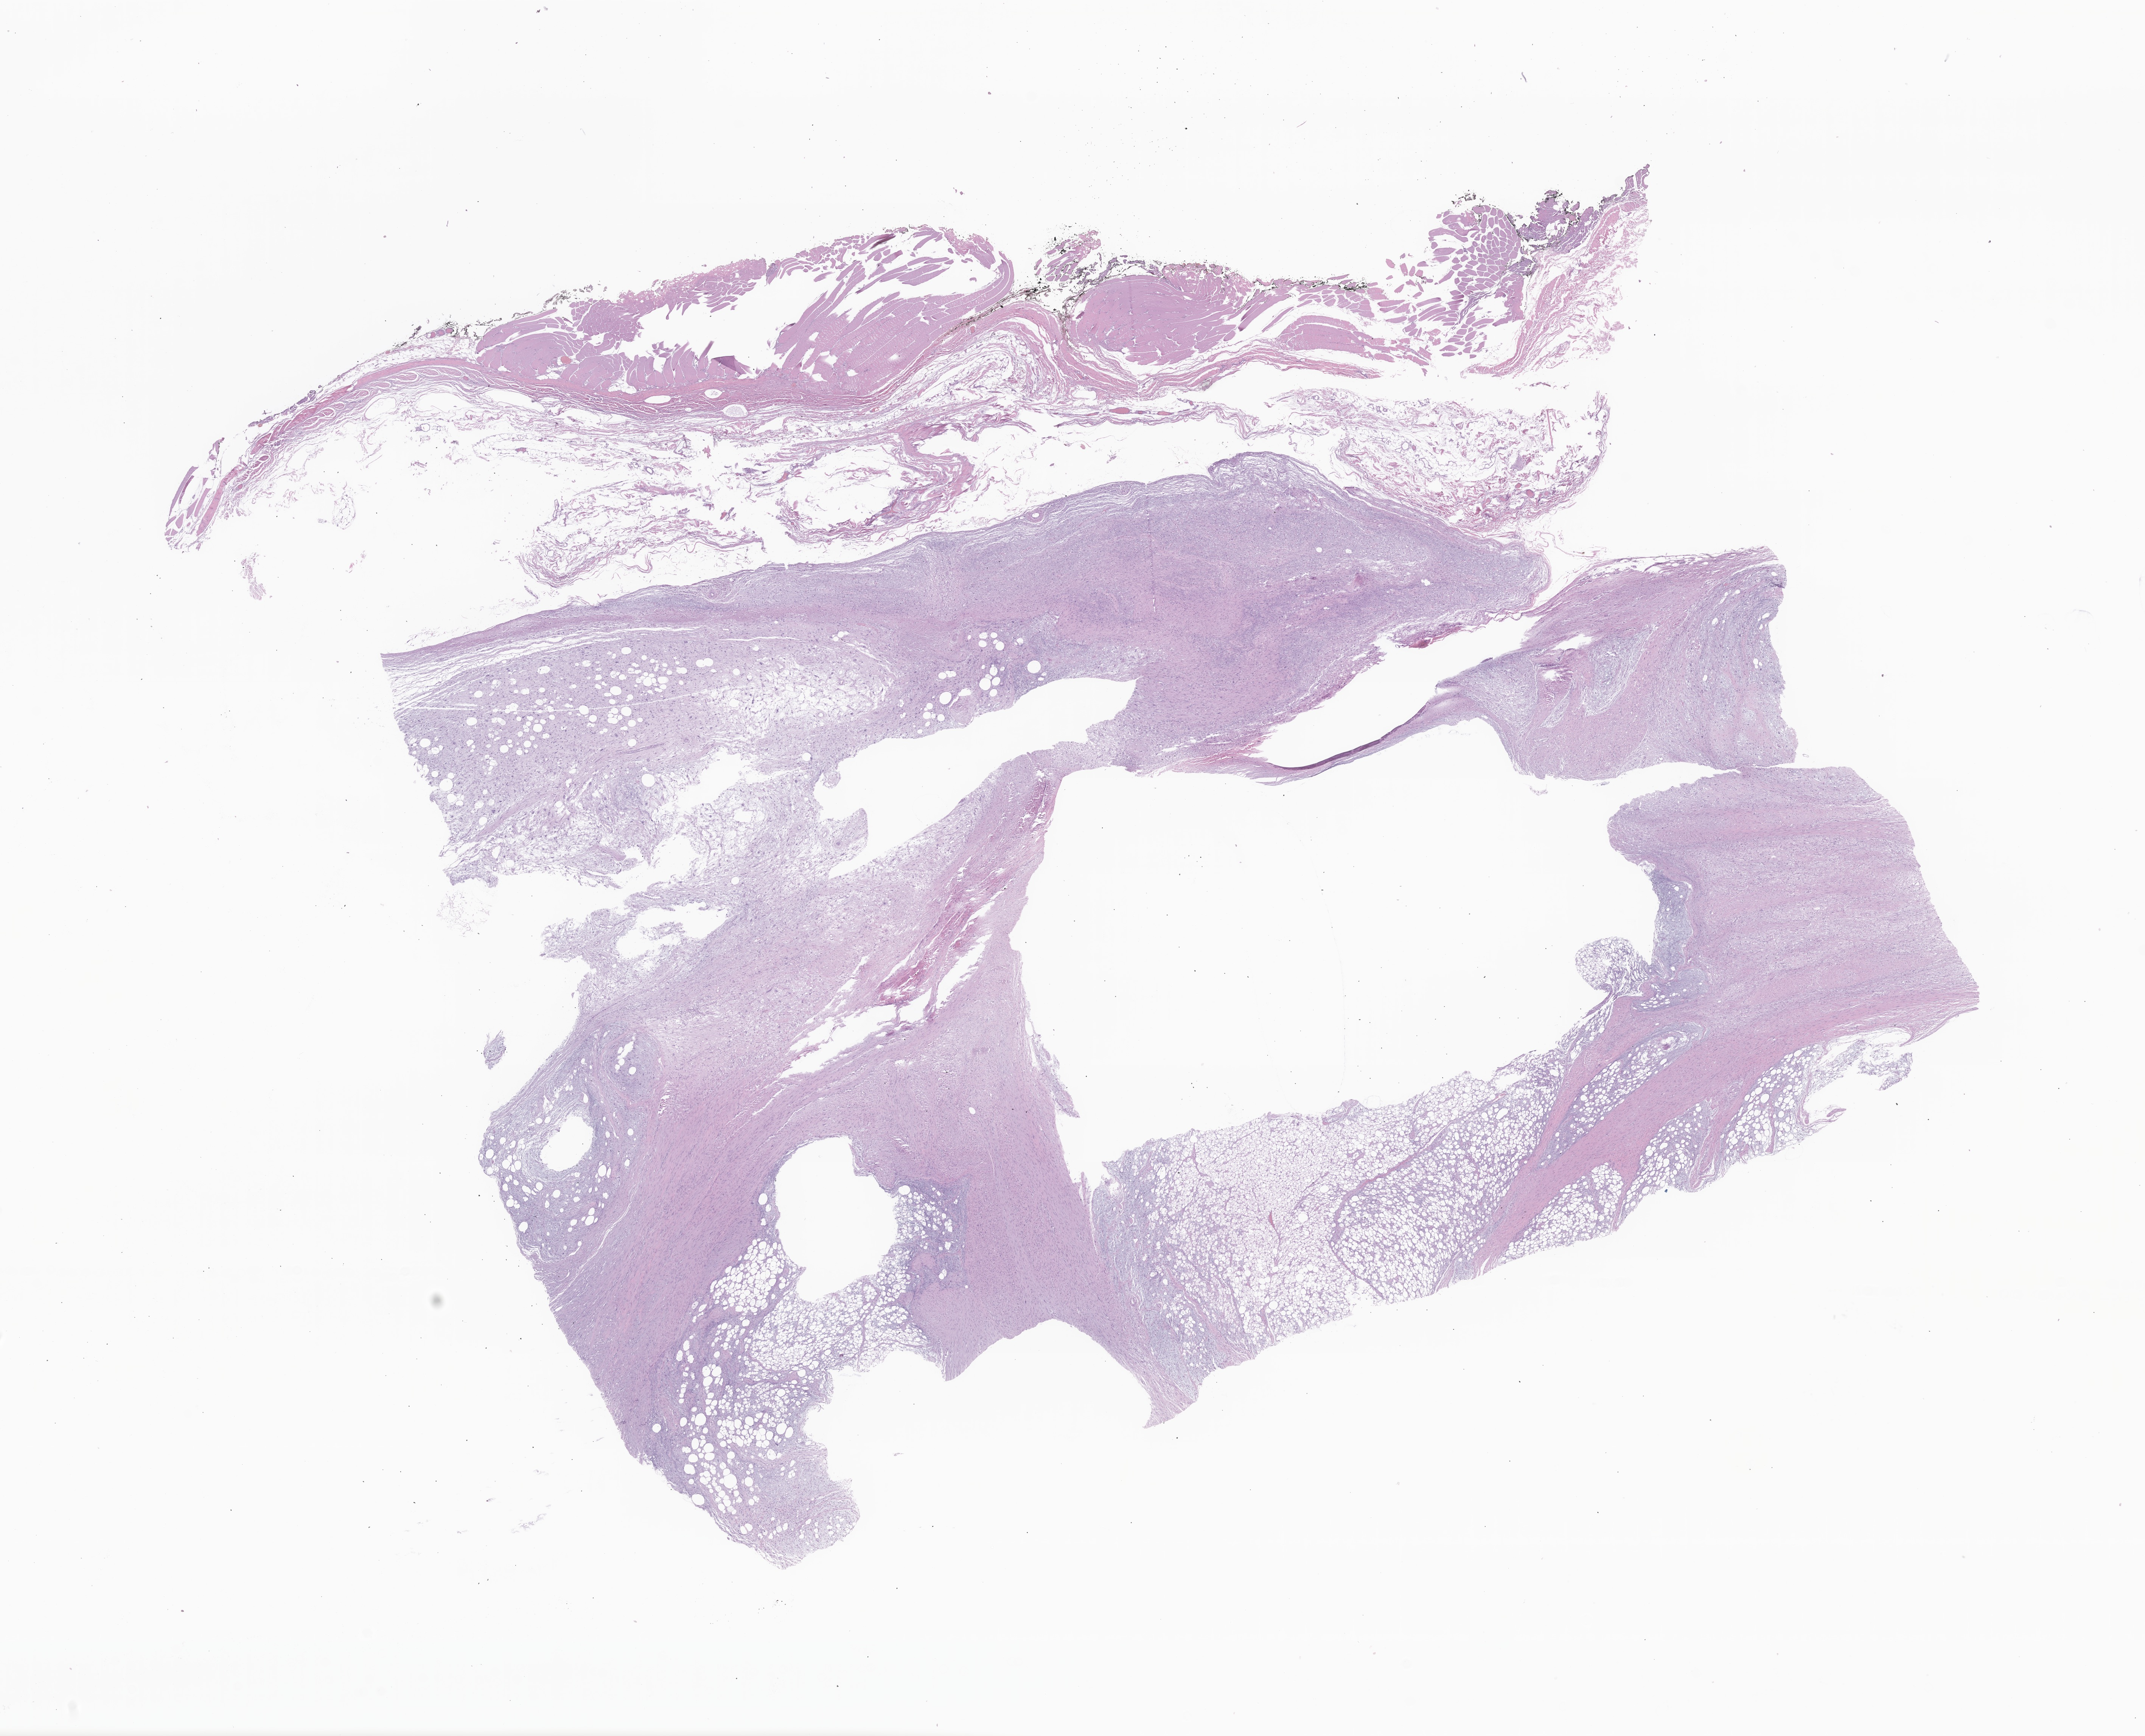
H&E whole-slide image of tumor tissue from the soft tissue of upper extremity, low-resolution overview of the scanned area, about 23.9 x 19.3 mm; formalin-fixed paraffin-embedded section. Patient female; age 228 months (19 years).
* recorded diagnosis: Pleomorphic liposarcoma